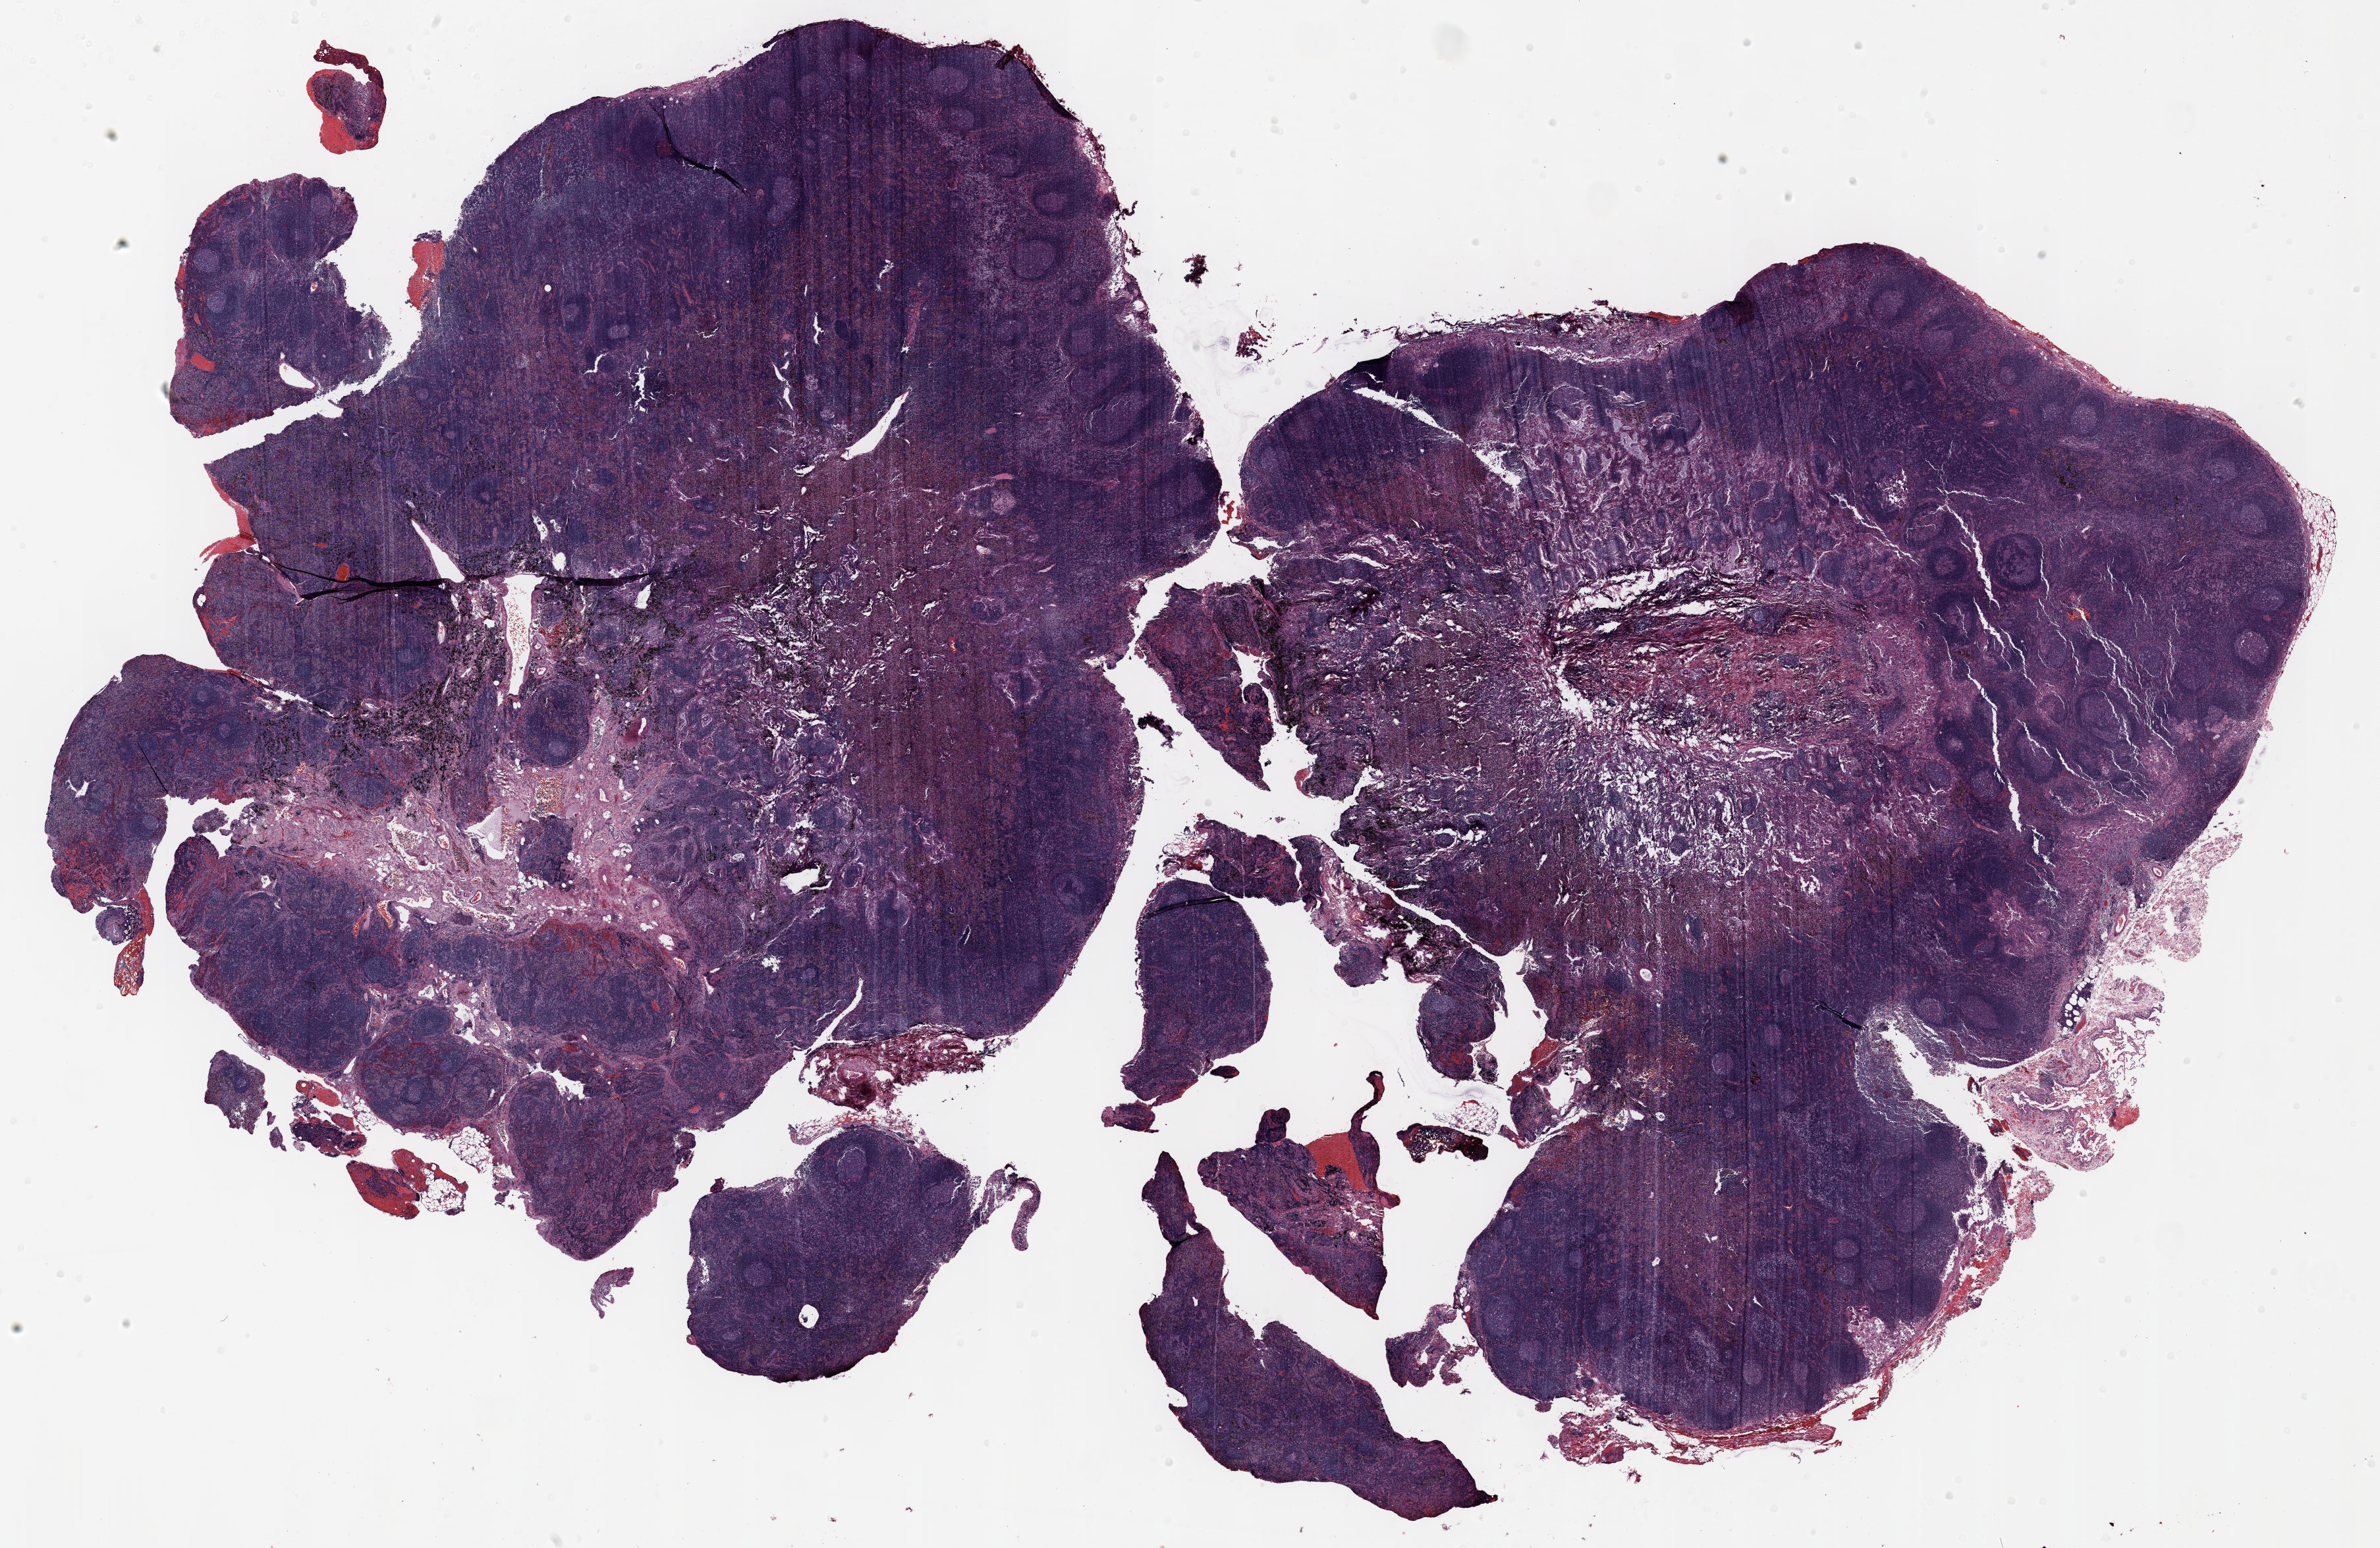
Whole-slide histology image, H&E-stained, a low-resolution overview of the entire scanned area, about 29.0 x 18.9 mm (from a 20x scan); FFPE section; lung tissue. Male patient, aged 66 at enrolment. Current smoker at enrolment. Grade: poorly differentiated (G3).
- tumour size (pathology): 50 mm
- stage (AJCC 6th edition): IIB
- primary tumour location (clinical record): right upper lobe
- participant's lung-cancer diagnosis: Squamous cell carcinoma, adenoid